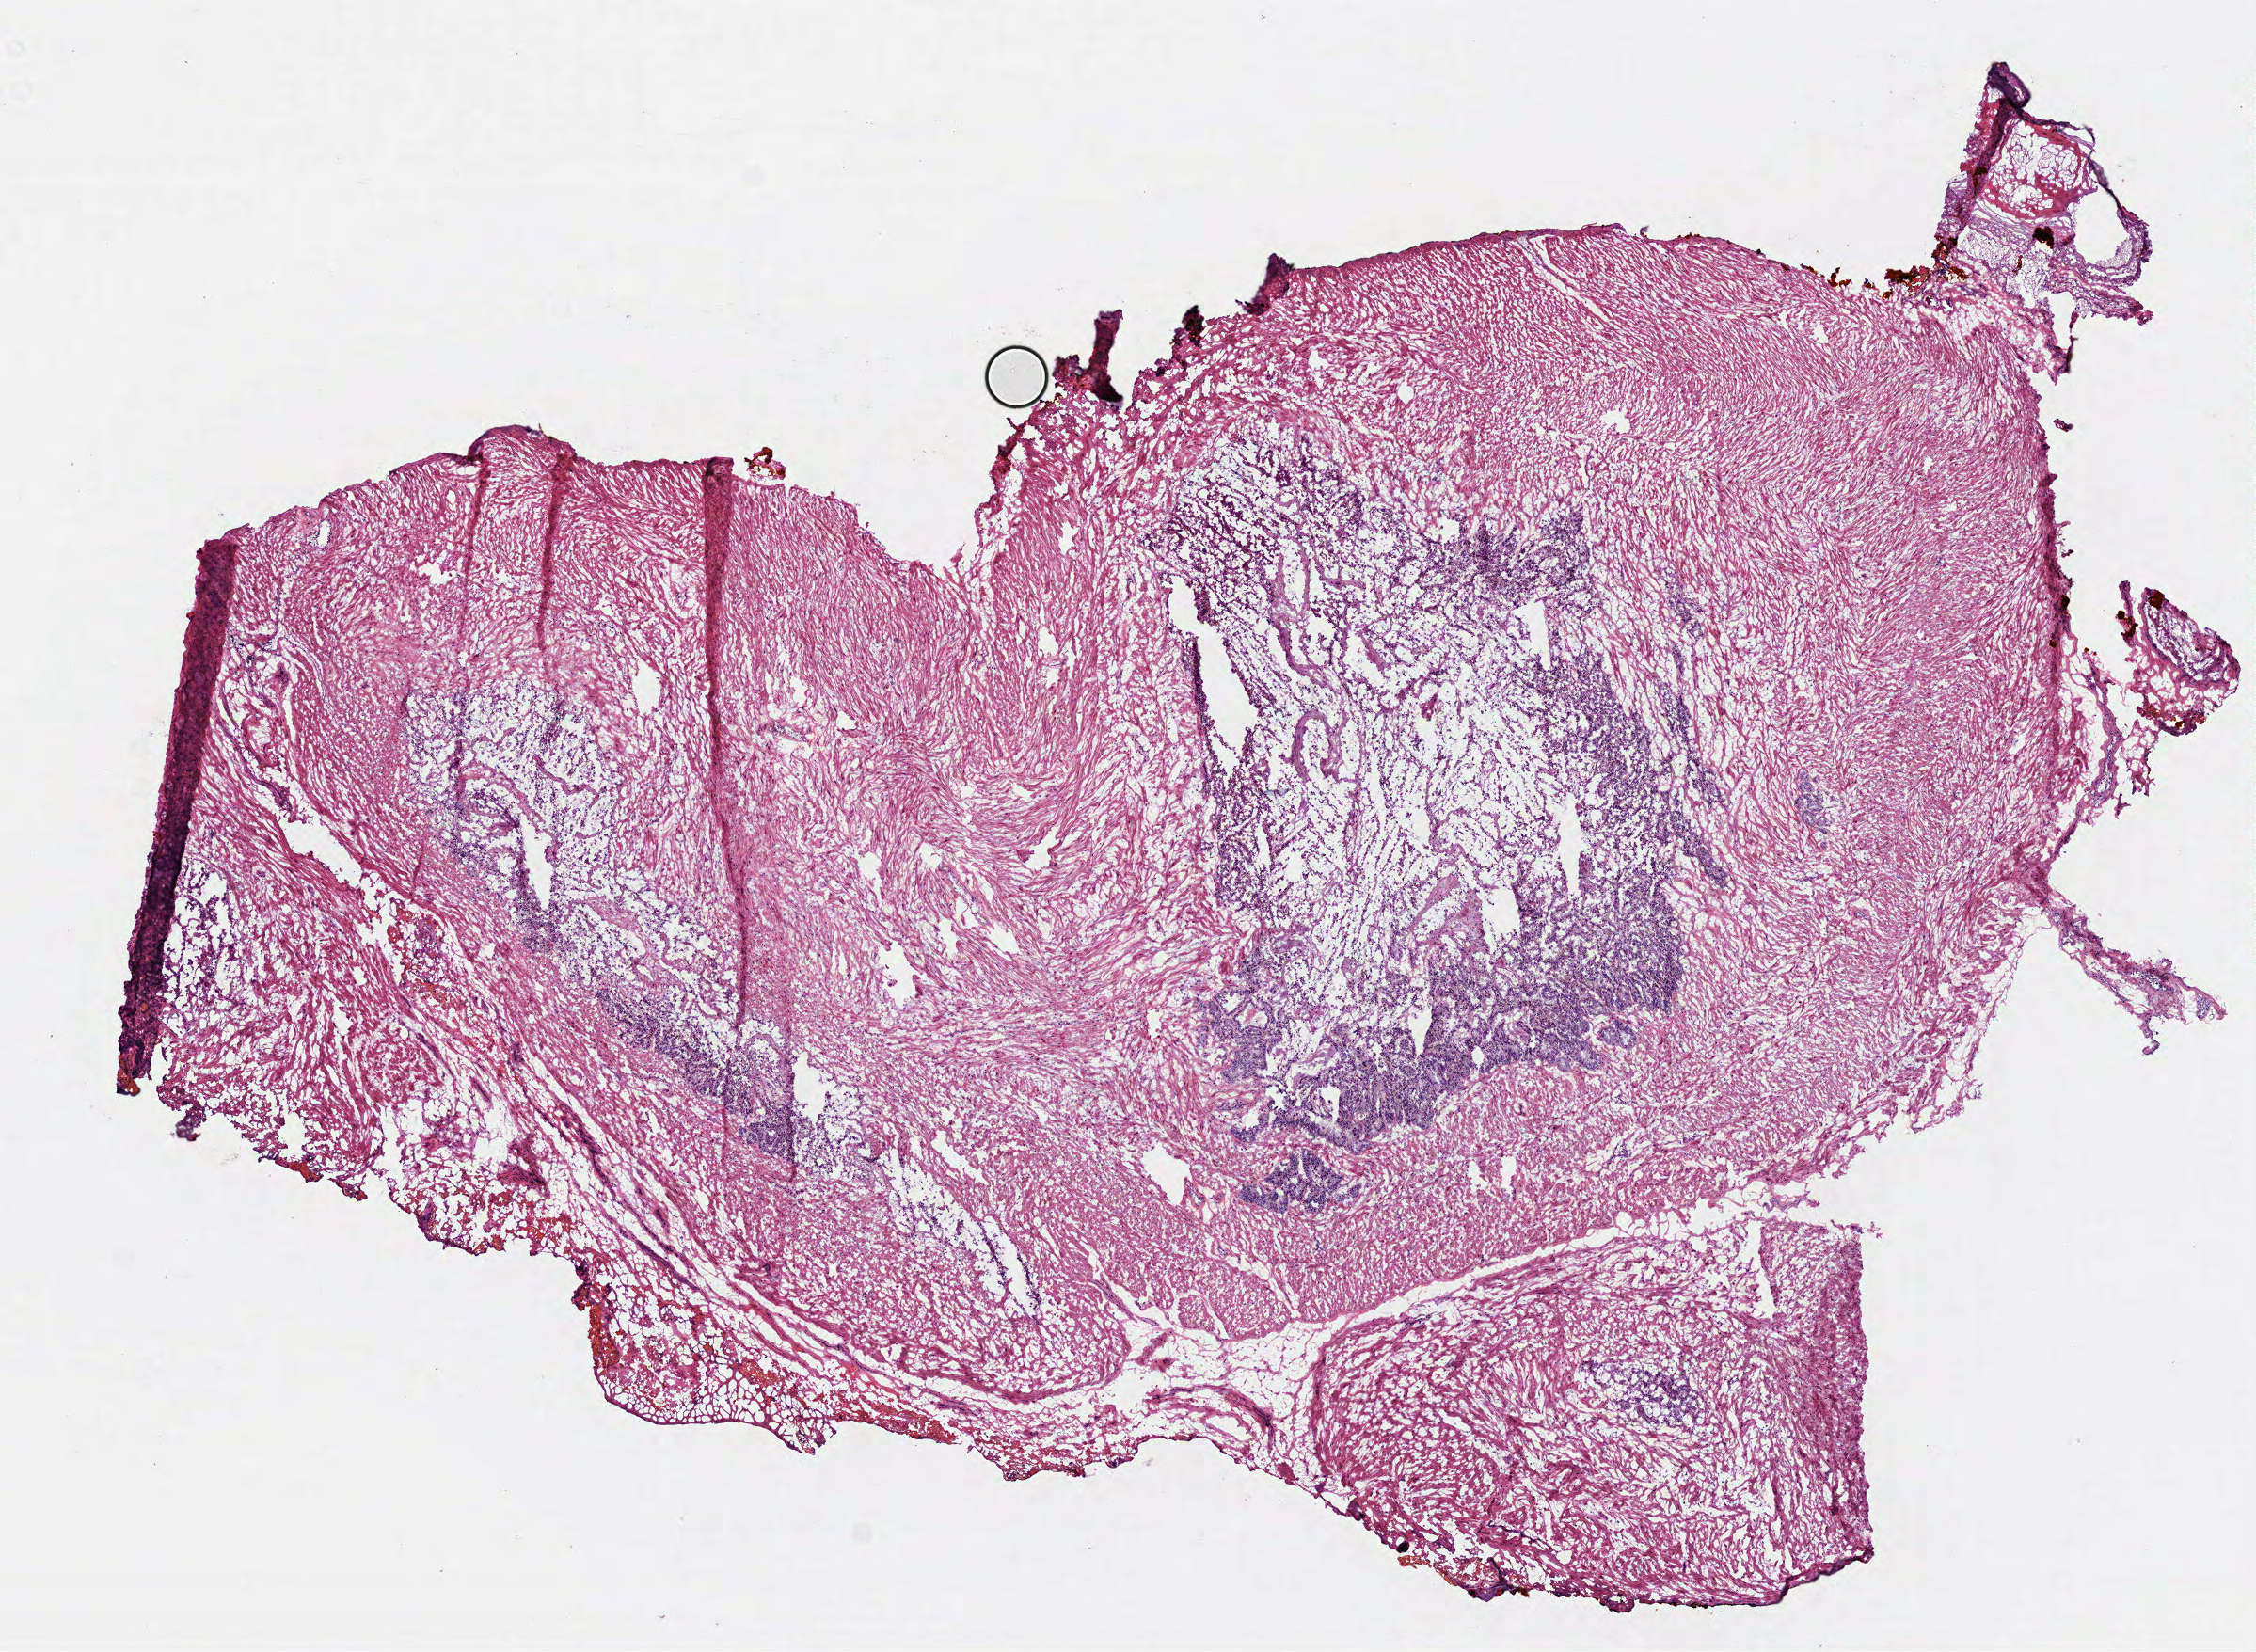
Whole-slide histology image, H&E-stained, shown as a low-resolution overview of the whole scanned area (about 9.7 x 7.1 mm, from a 40x scan); frozen section from the top of the tissue portion; prostate, solid tissue normal (non-tumour tissue) sample. Male patient; age at initial diagnosis 53 years.
This section: solid tissue normal sample (biorepository sample class). Patient diagnosis: Acinar cell carcinoma (prostate gland).